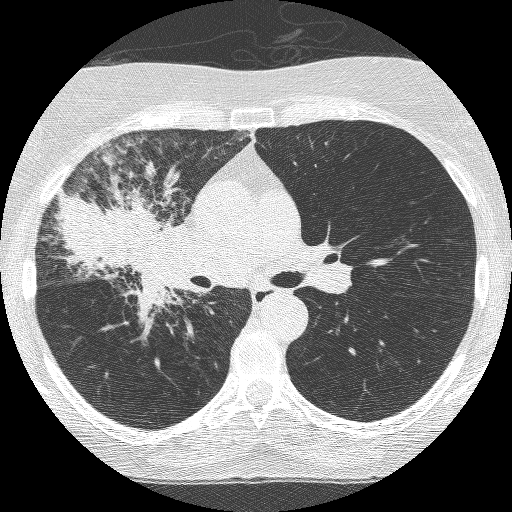
Axial slice from a low-dose chest CT screening exam, third screening round (two years after baseline), lung window (W 1500 / L -600 HU), 1.25 mm slice thickness, 120 kVp, 512 × 512 image matrix. Female, age 64 years at enrolment. Former smoker at enrolment.
- Lesion marked by an expert reader, bounding box <73,192,203,323> (left, top, right, bottom; pixels).
- Screening reader's record for this exam (one nodule recorded; not confirmed to be the boxed lesion): non-calcified nodule or mass ≥4 mm, right upper lobe, 49 × 43 mm, spiculated (stellate) margins, soft tissue attenuation, pre-existing on the prior screen: yes; interval growth: yes.
- Participant outcome: lung cancer diagnosed 7 days after this screen — adenocarcinoma, NOS, right upper lobe, right middle lobe, right hilum, stage IV (AJCC 6th edition), 85 mm at pathology.